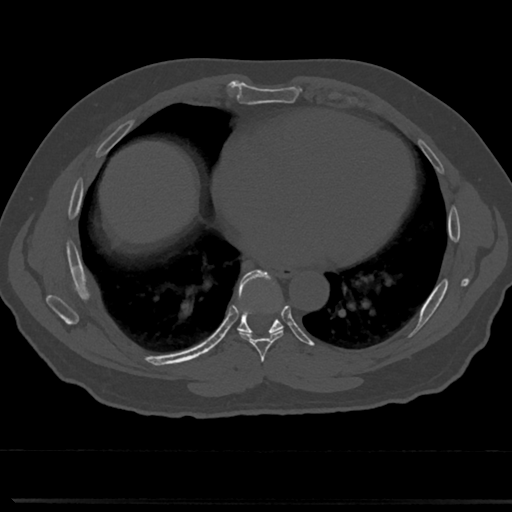
CT including the spine, one axial slice; position 383 of 817 along the scan axis; 120 kVp; bone window (W 1800 / L 400 HU); 0.5 mm slice thickness; 512 × 512 image matrix. Male patient, age 61 years. From the clinical record (not read from this slice): primary cancer: prostate.
Annotated regions visible in this slice (semi-automatically segmented with operator editing):
- T6 vertebra: bounding box [x1, y1, x2, y2] px = [260, 368, 267, 377]
- T7 vertebra: [229, 273, 306, 352]